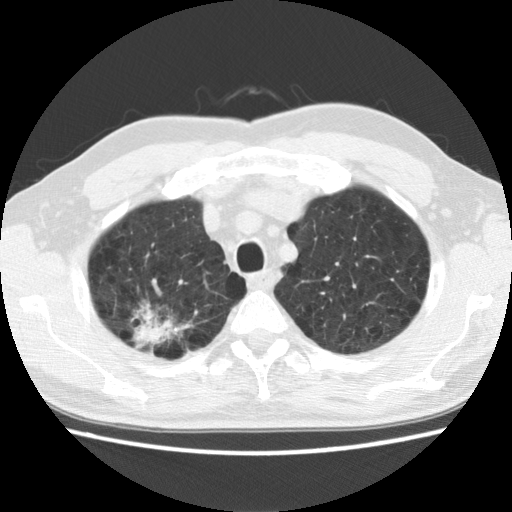
Chest CT (low-dose screening protocol), one axial image, baseline screening round, lung window (W 1500 / L -600 HU), 2.5 mm slice thickness, standard (soft-tissue) reconstruction kernel (STANDARD), slice 29 of 142 in the series. Male, age 64 years at enrolment. Former smoker at enrolment.
Expert-annotated lung lesion, bounding box <111,291,199,364> (left, top, right, bottom; pixels). Screening reader's record for this exam (one nodule recorded; not confirmed to be the boxed lesion): non-calcified nodule or mass ≥4 mm, right upper lobe, 39 × 31 mm, spiculated (stellate) margins, mixed attenuation. Official screen result: positive, change unspecified: nodule(s) >= 4 mm or enlarging nodule(s), mass(es), or other non-specific abnormalities suspicious for lung cancer. Participant outcome: lung cancer diagnosed 74 days after this screen — adenocarcinoma, NOS, right upper lobe, moderately differentiated (G2), stage IB (AJCC 6th edition), 40 mm at pathology.